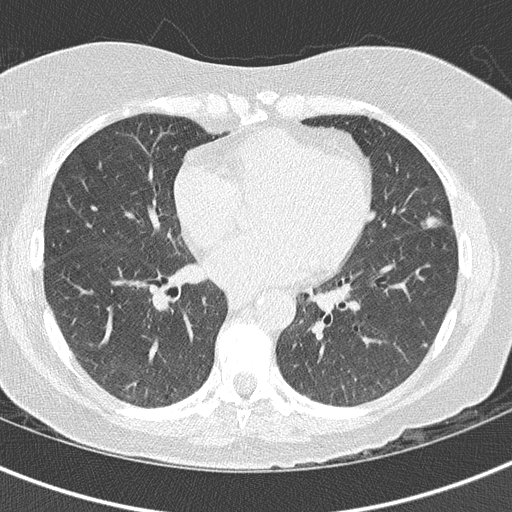
Chest CT (low-dose screening protocol), one axial image; third screening round (two years after baseline); lung window (W 1500 / L -600 HU); 2 mm slice thickness; lung (sharp) reconstruction kernel (B50f); 120 kVp; slice 78 of 158 in the series. Female participant, aged 63 years at enrolment. Current smoker at enrolment.
• Expert-annotated lung lesion, bounding box (x1, y1, x2, y2) in pixels: (384, 196, 454, 247).
• The screening reader recorded 5 non-calcified nodules or masses ≥4 mm on this exam; which of them this box marks is not recorded.
• Participant outcome: lung cancer diagnosed 35 days after this screen — bronchiolo-alveolar adenocarcinoma, NOS, lingula, stage IA (AJCC 6th edition), 14 mm at pathology.